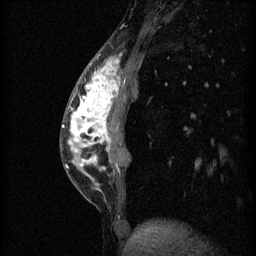
Breast MRI (dynamic contrast-enhanced), one sagittal slice. Slice 17 of 60 in the series (ordered by position). 3 images stored at this slice position (order not interpretable as contrast timing). 1.5 T. TE 4.2 ms, TR 11 ms. 256 × 256 image matrix, field of view 180 × 180 mm. Patient: female, 40 years.
Outlined on this slice (semi-automatically segmented with operator editing):
- analysis volume of interest (the breast-tissue region the enhancement analysis was run in; not a lesion): bounding box <61,46,131,203> (left, top, right, bottom; pixels)
- tumour enhancement mask (voxels above the 70 % enhancement threshold inside the analysis volume of interest): <63,58,121,169>